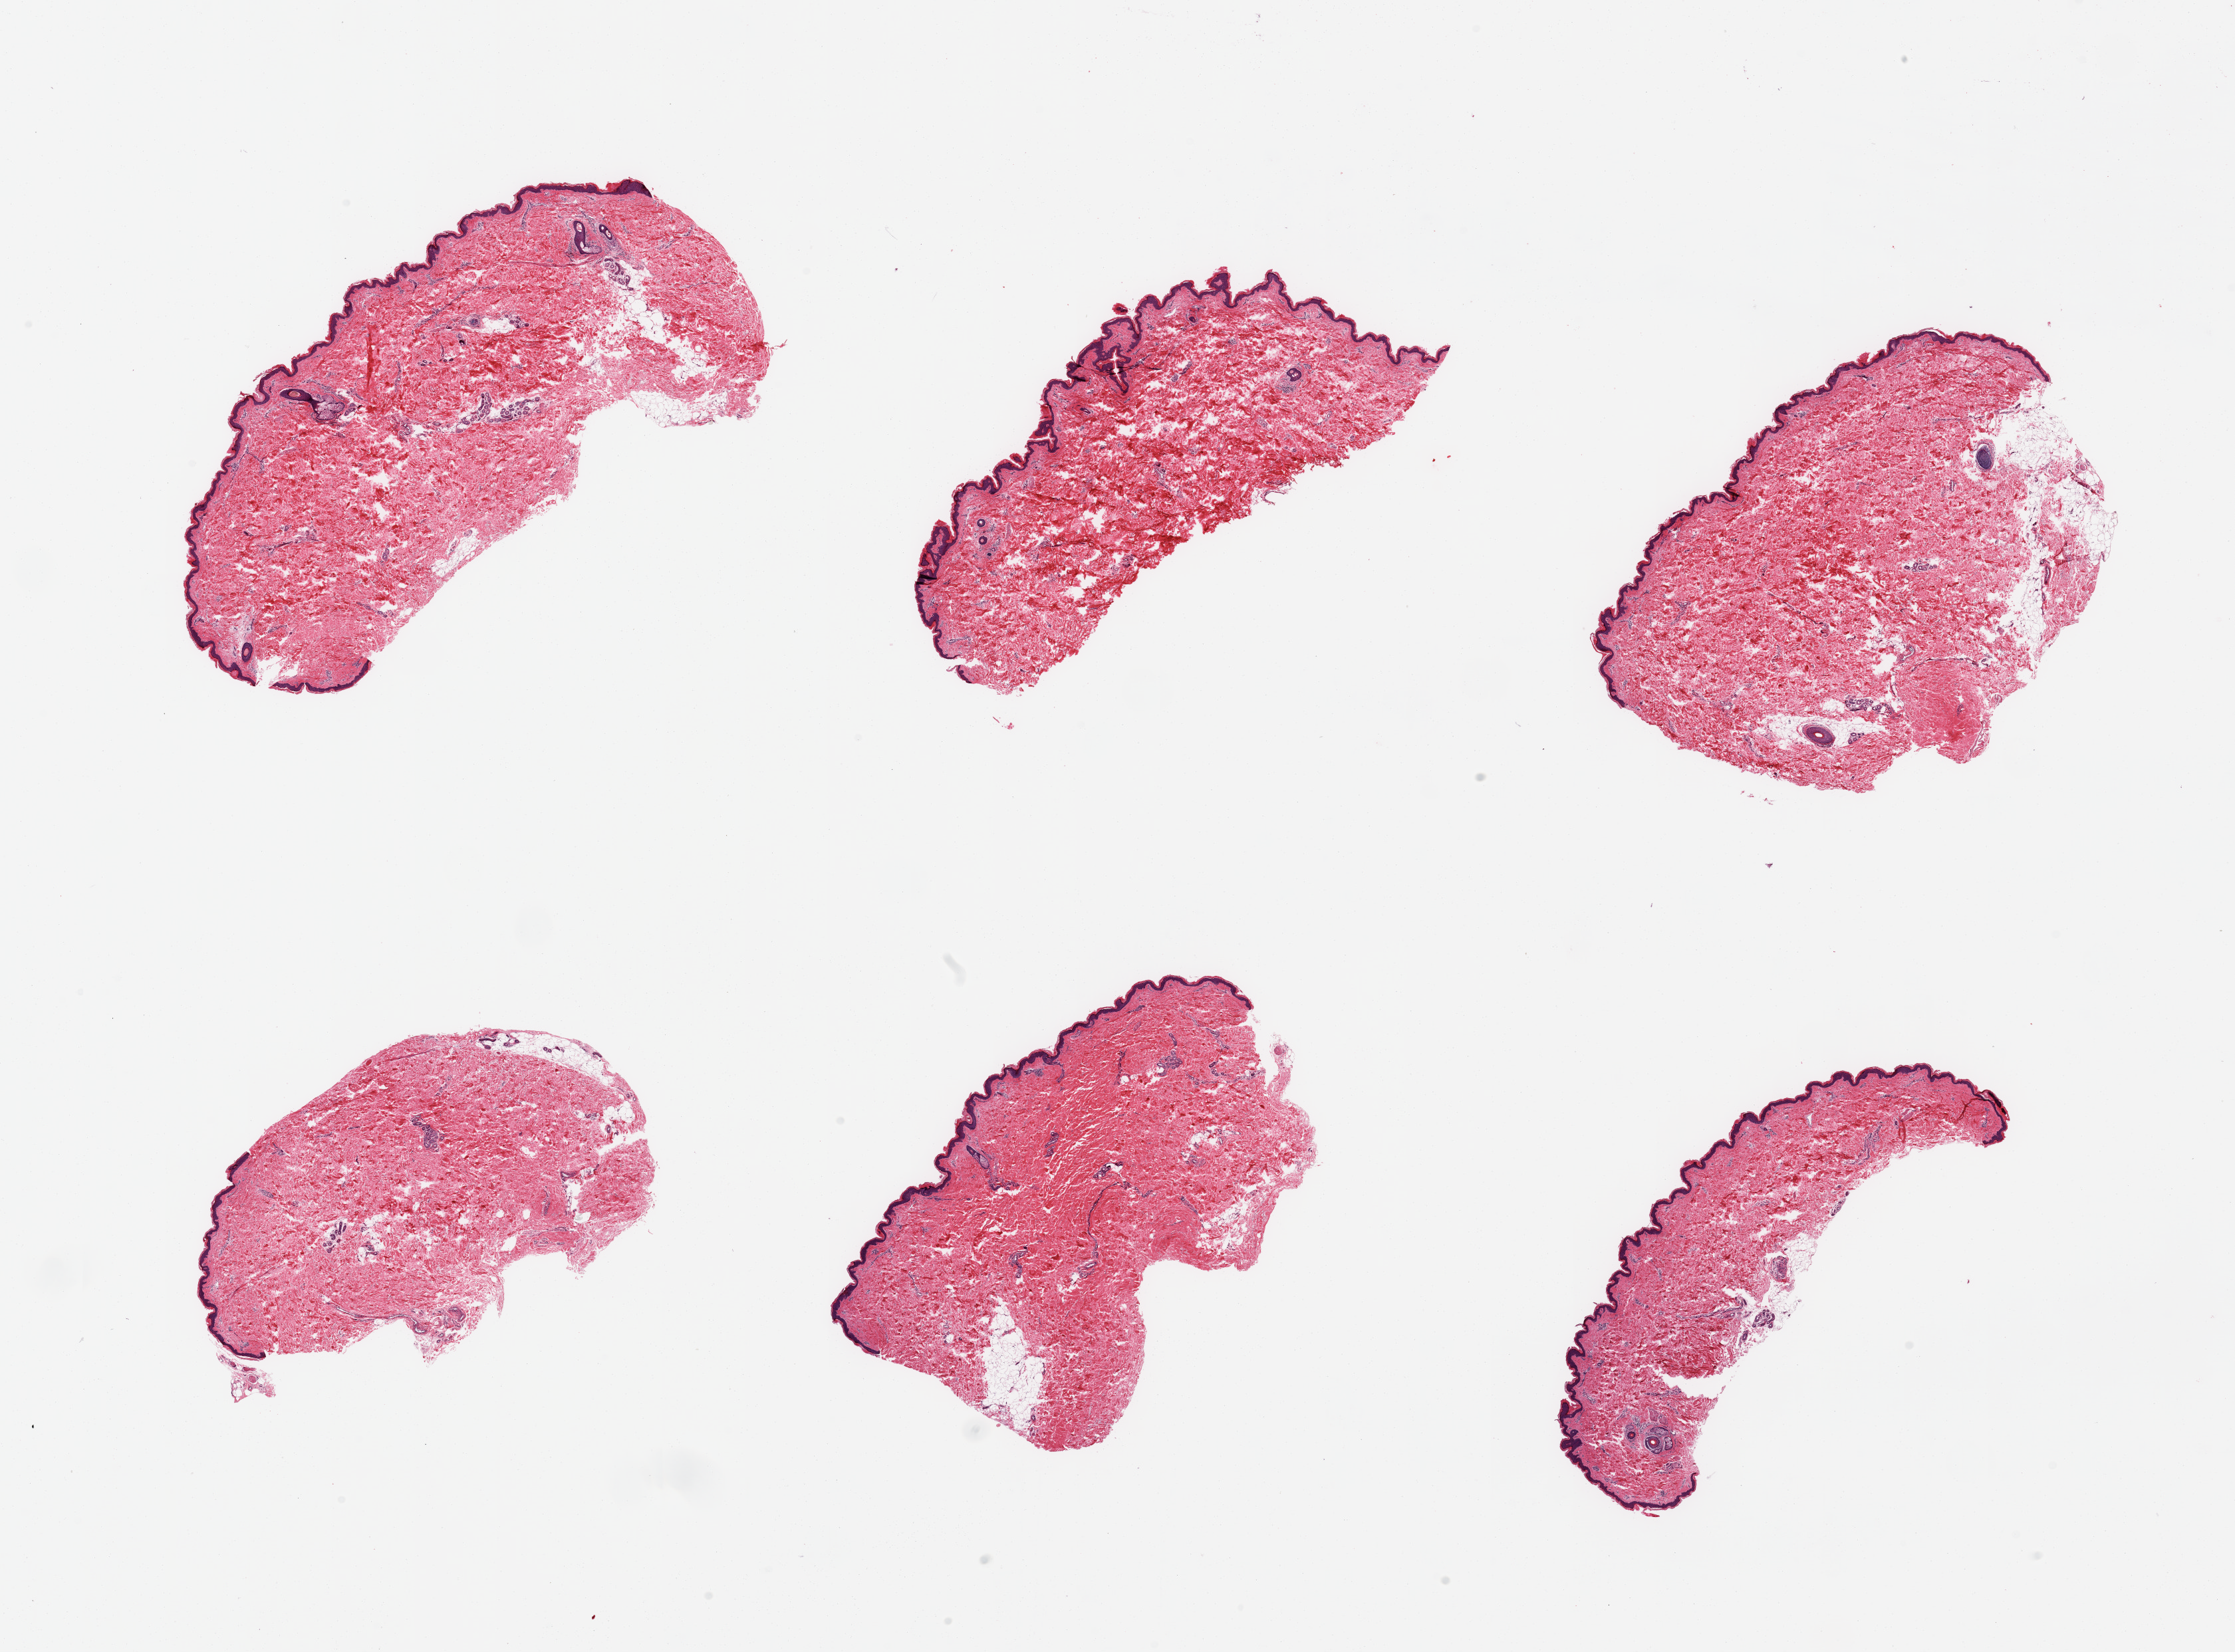
Whole-slide image, haematoxylin and eosin stain, brightfield — low-resolution overview of the scanned area, about 26.6 x 19.7 mm (slide scanned at 20x), PAXgene-fixed, paraffin-embedded tissue, target tissue: skin of lower leg, tissue donor sample. Donor: male.
Pathologist's review note for this sample: 6 pieces; 5% dermal fat; well trimmed.